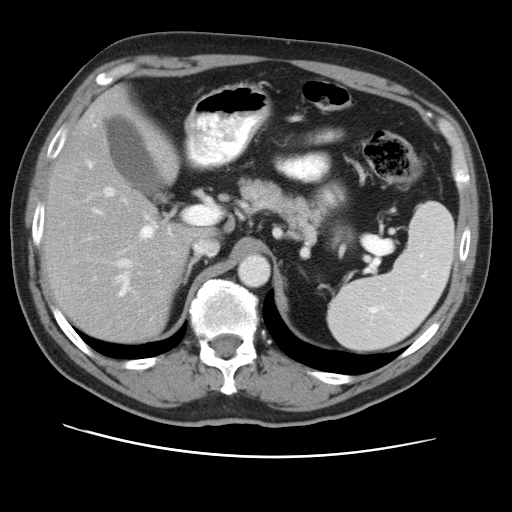
Contrast-enhanced abdominal CT, one axial slice; position 30 of 49 along the scan axis; reconstruction kernel STANDARD; 120 kVp; intravenous contrast given; soft-tissue window (W 400 / L 40 HU); 5 mm slice thickness; 512 × 512 image matrix, field of view 374 × 374 mm. Male patient, age 59 years. From the clinical record (not read from this slice): diagnosis: colorectal cancer liver metastases, imaged before liver resection; multiple liver metastases: yes; largest metastasis: 6.3 cm; chemotherapy before resection: yes.
Annotated regions visible in this slice (expert manual segmentation):
- hepatic veins: box from (x=105, y=187) to (x=215, y=255) px
- liver: (x=46, y=91)–(x=206, y=342)
- planned liver remnant (the part of the liver to remain after resection): (x=46, y=92)–(x=206, y=342)
- portal vein (with intrahepatic branches): (x=85, y=159)–(x=220, y=295)